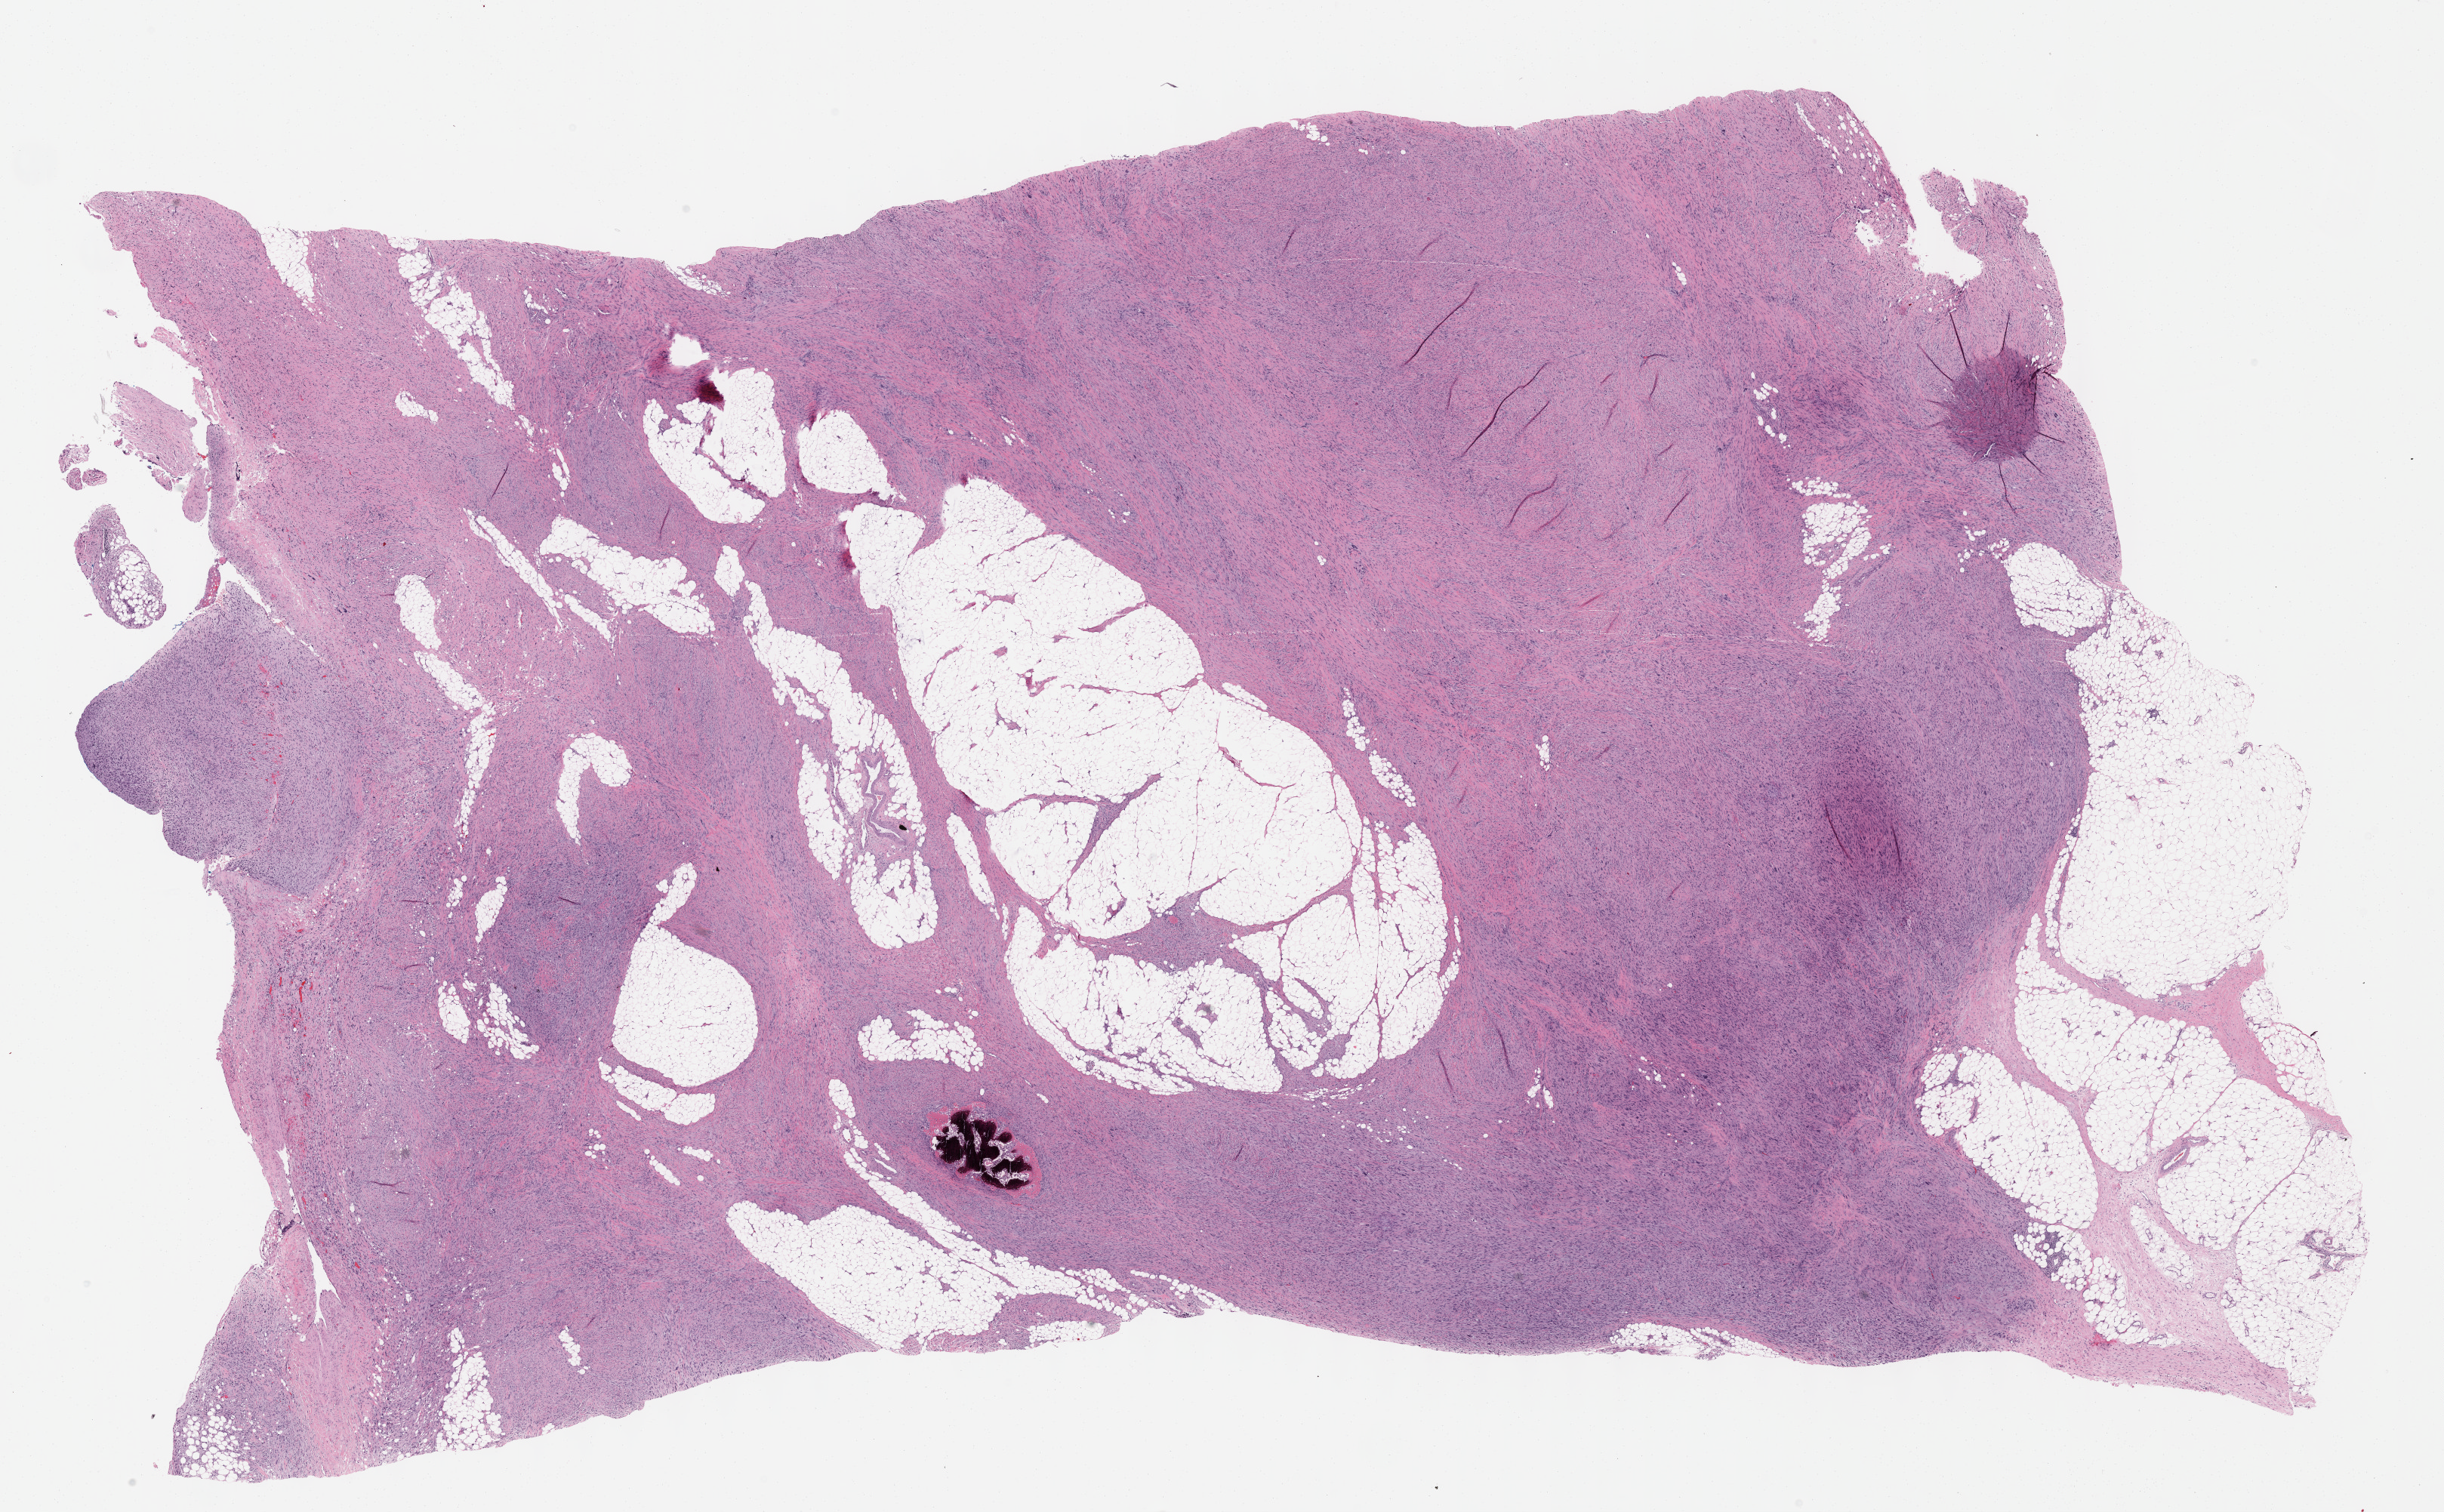
H&E whole-slide image, shown as a low-resolution overview of the whole scanned area (about 26.2 x 16.2 mm, from a 40x scan), FFPE section, connective, subcutaneous and other soft tissues, primary tumour sample. Patient: male, age at initial diagnosis 76 years.
Histologic diagnosis: Malignant fibrous histiocytoma (connective, subcutaneous and other soft tissues of thorax).